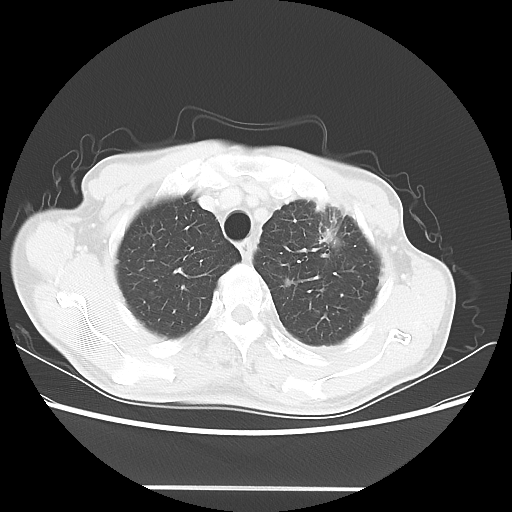
Chest CT, one axial slice. Slice 49 of 60 in the series (ordered by position). 100 kVp. Lung window (W 1500 / L -600 HU). 5 mm slice thickness. 512 × 512 image matrix, field of view 367 × 367 mm. Male patient, age 74 years. Case-level facts recorded for this patient, not image findings: clinical TNM (as recorded): T1c N0 M1a.
Outlined on this slice (bounding box drawn by a radiologist):
- lung tumour (recorded histology: adenocarcinoma): bounding box [x1, y1, x2, y2] px = [317, 220, 344, 246]